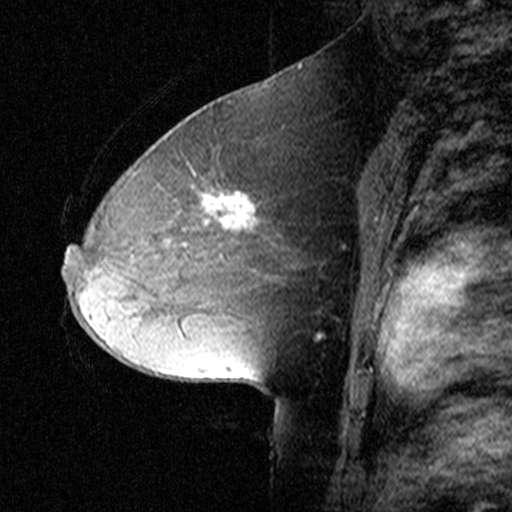
Breast MRI (dynamic contrast-enhanced), one sagittal slice. Slice 20 of 44 in the series (ordered by position). Dynamic contrast-enhanced study with each time point stored as its own series, time point 2 of 3 at this slice position (early post-contrast, ordered by acquisition time). 1.5 T. TE 4.5 ms, TR 11 ms. 3 mm slice thickness. 512 × 512 image matrix, field of view 200 × 200 mm. Female patient, age 50 years. Case-level facts recorded for this patient, not image findings: setting: breast cancer imaged before/during neoadjuvant chemotherapy; receptor status: HR-positive, HER2-negative.
Outlined on this slice (semi-automatically segmented with operator editing):
- analysis volume of interest (the breast-tissue region the enhancement analysis was run in; not a lesion): box from (x=154, y=164) to (x=313, y=287) px
- tumour enhancement mask (voxels above the 90 % enhancement threshold inside the analysis volume of interest): (x=206, y=194)–(x=252, y=230)